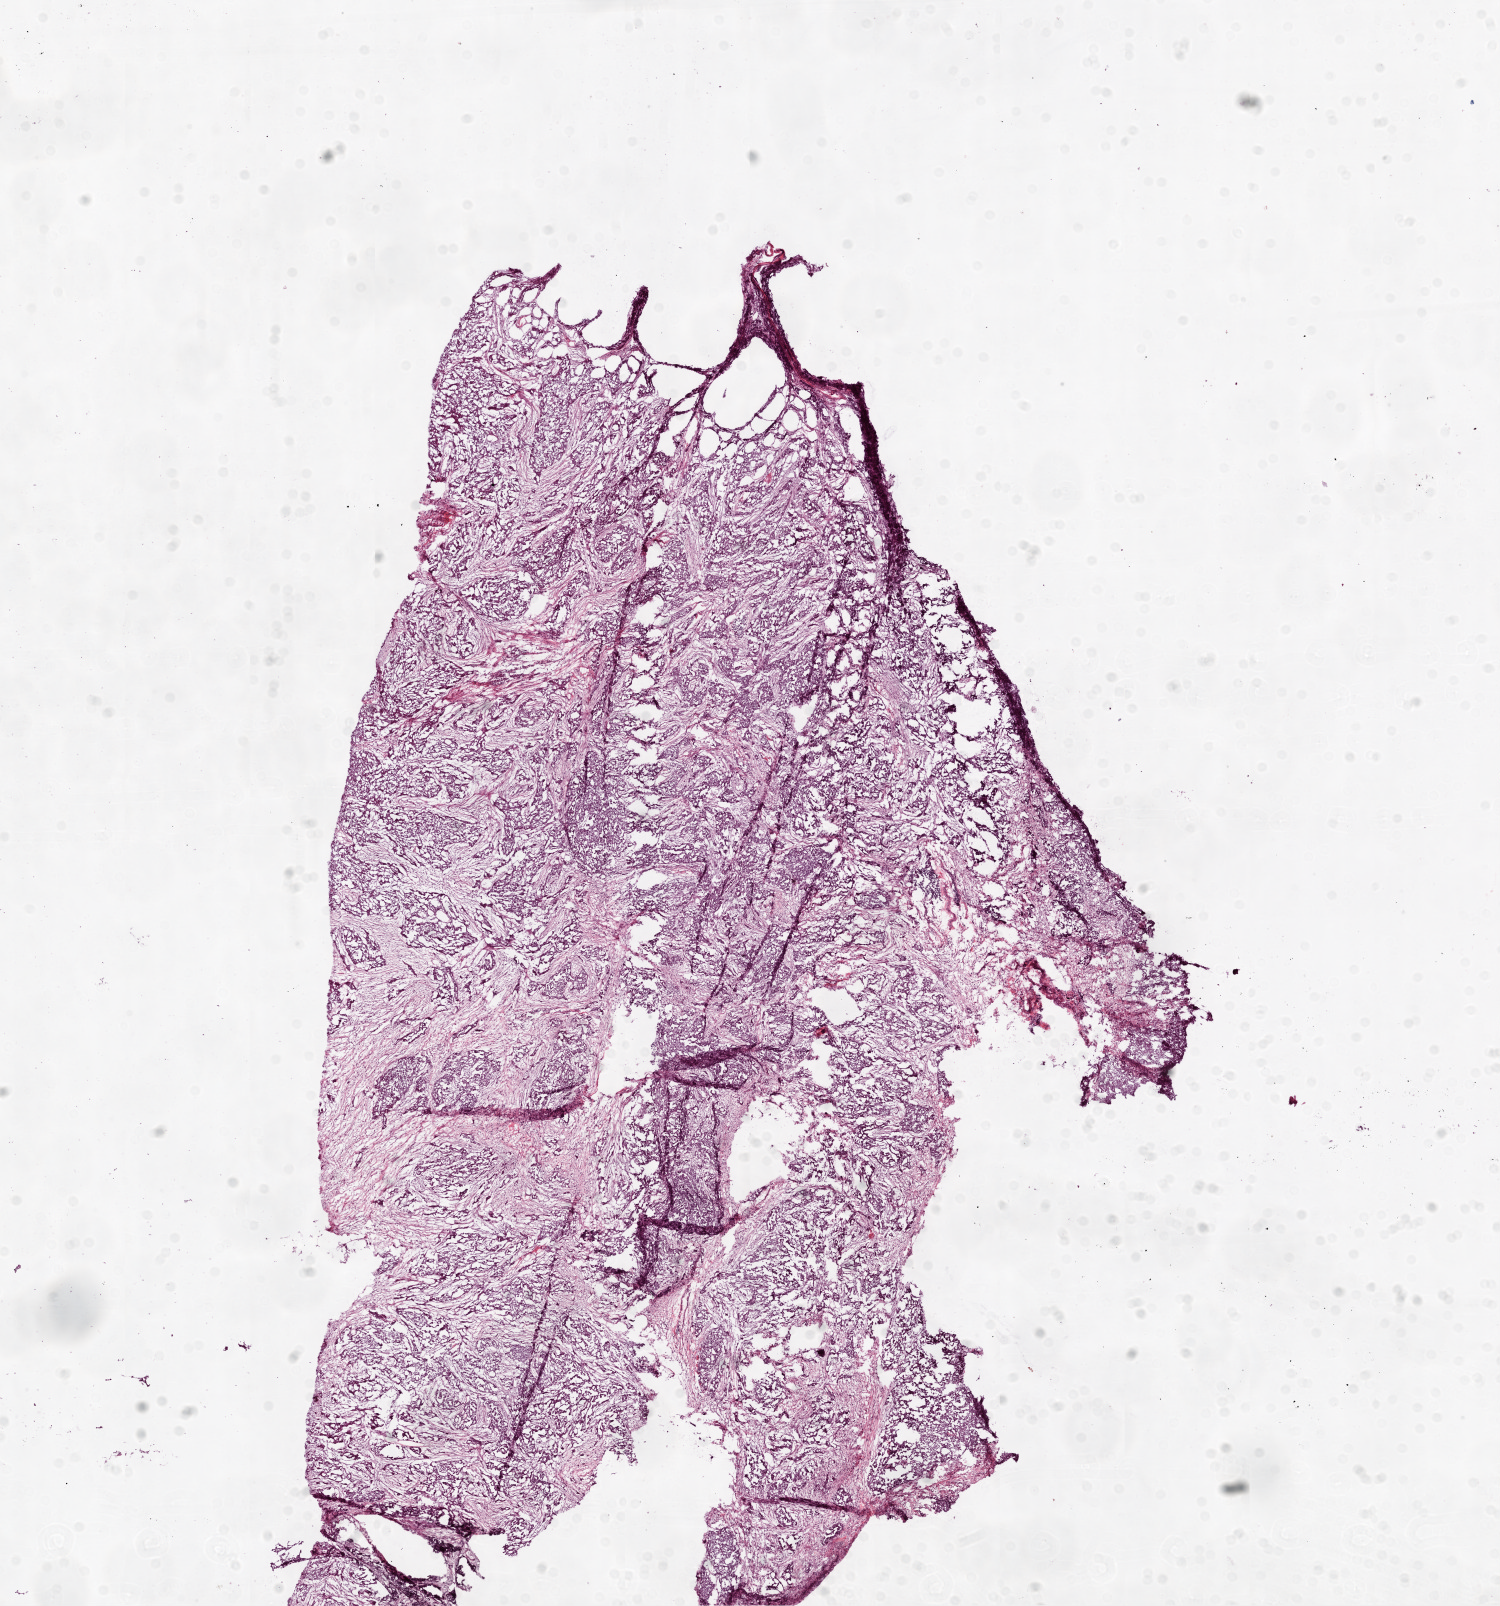
Whole-slide histology image, H&E-stained, shown as a low-resolution overview of the whole scanned area (about 12.0 x 12.9 mm, acquisition: 20x scan). Frozen section from the top of the tissue portion. Ovary, primary tumour sample. Female patient; age at initial diagnosis 63 years. Histologic grade: G3 (poorly differentiated). Pathologist review of this section (percent, as recorded): tumour cells 90%, tumour nuclei 90%, normal cells 0%, stromal cells 10%, necrosis 0%.
- pathologic diagnosis: Serous cystadenocarcinoma, NOS
- FIGO stage: IIIC